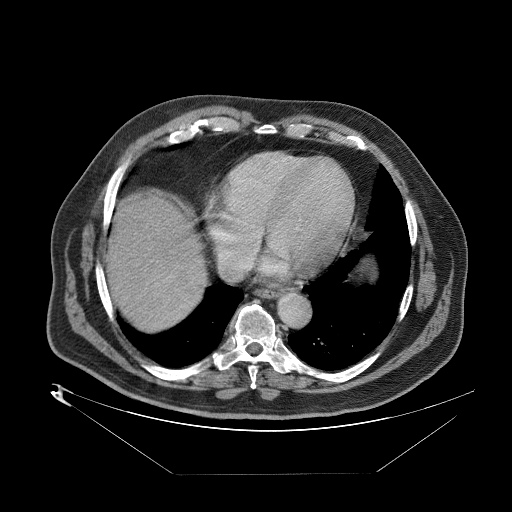
Contrast-enhanced abdominal CT (liver protocol), one axial slice. Position 78 of 89 along the scan axis. Reconstruction kernel STANDARD. One of 2 acquisitions stored at this slice position. Soft-tissue window (W 400 / L 40 HU). 2.5 mm slice thickness. 512 × 512 image matrix, field of view 480 × 480 mm. Case-level facts recorded for this patient, not image findings: diagnosis: hepatocellular carcinoma (patient treated with transarterial chemoembolisation; whether this scan precedes or follows treatment is not stated here); TNM stage (as recorded): Stage-II; Child-Pugh class: B; tumour differentiation: moderately differentiated; tumour nodularity: multinodular.
Annotated regions visible in this slice (semi-automatic segmentation, software-assisted and operator-edited):
- abdominal aorta: bounding box <276,291,311,326> (left, top, right, bottom; pixels)
- liver parenchyma outside the tumour (the mass and vessels are separate outlines, so this box may not span the whole liver): <108,192,202,321>
- mass: <162,262,197,297>
- liver vessels: <184,297,186,300>